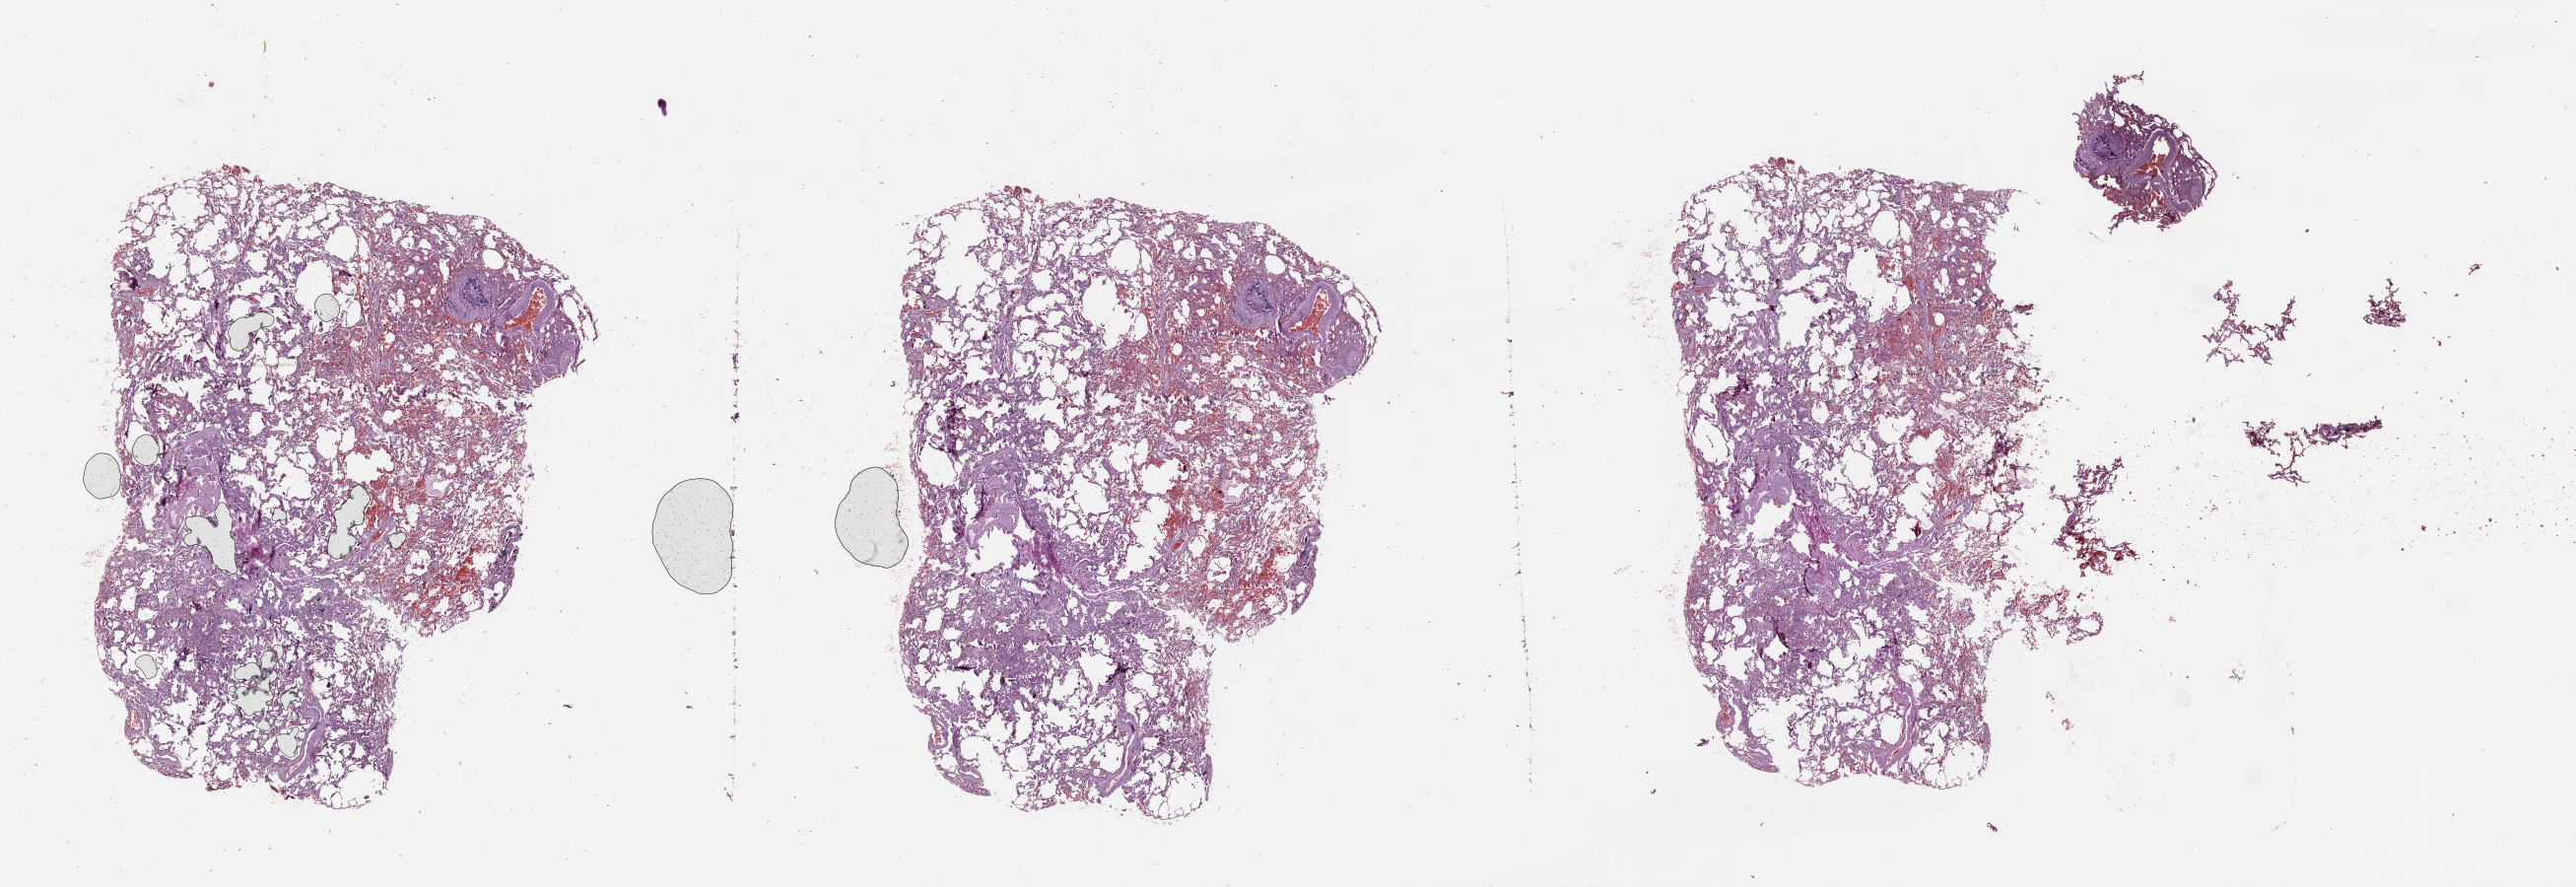
H&E whole-slide image — shown as a low-resolution overview of the whole scanned area (about 42.1 x 14.5 mm, slide scanned at 20x); normal (non-tumour) tissue sample, lung. Female, 62 y/o.
This section: normal (non-tumour) tissue from the same patient. Patient diagnosis (cohort enrolment): squamous cell carcinoma (lung).